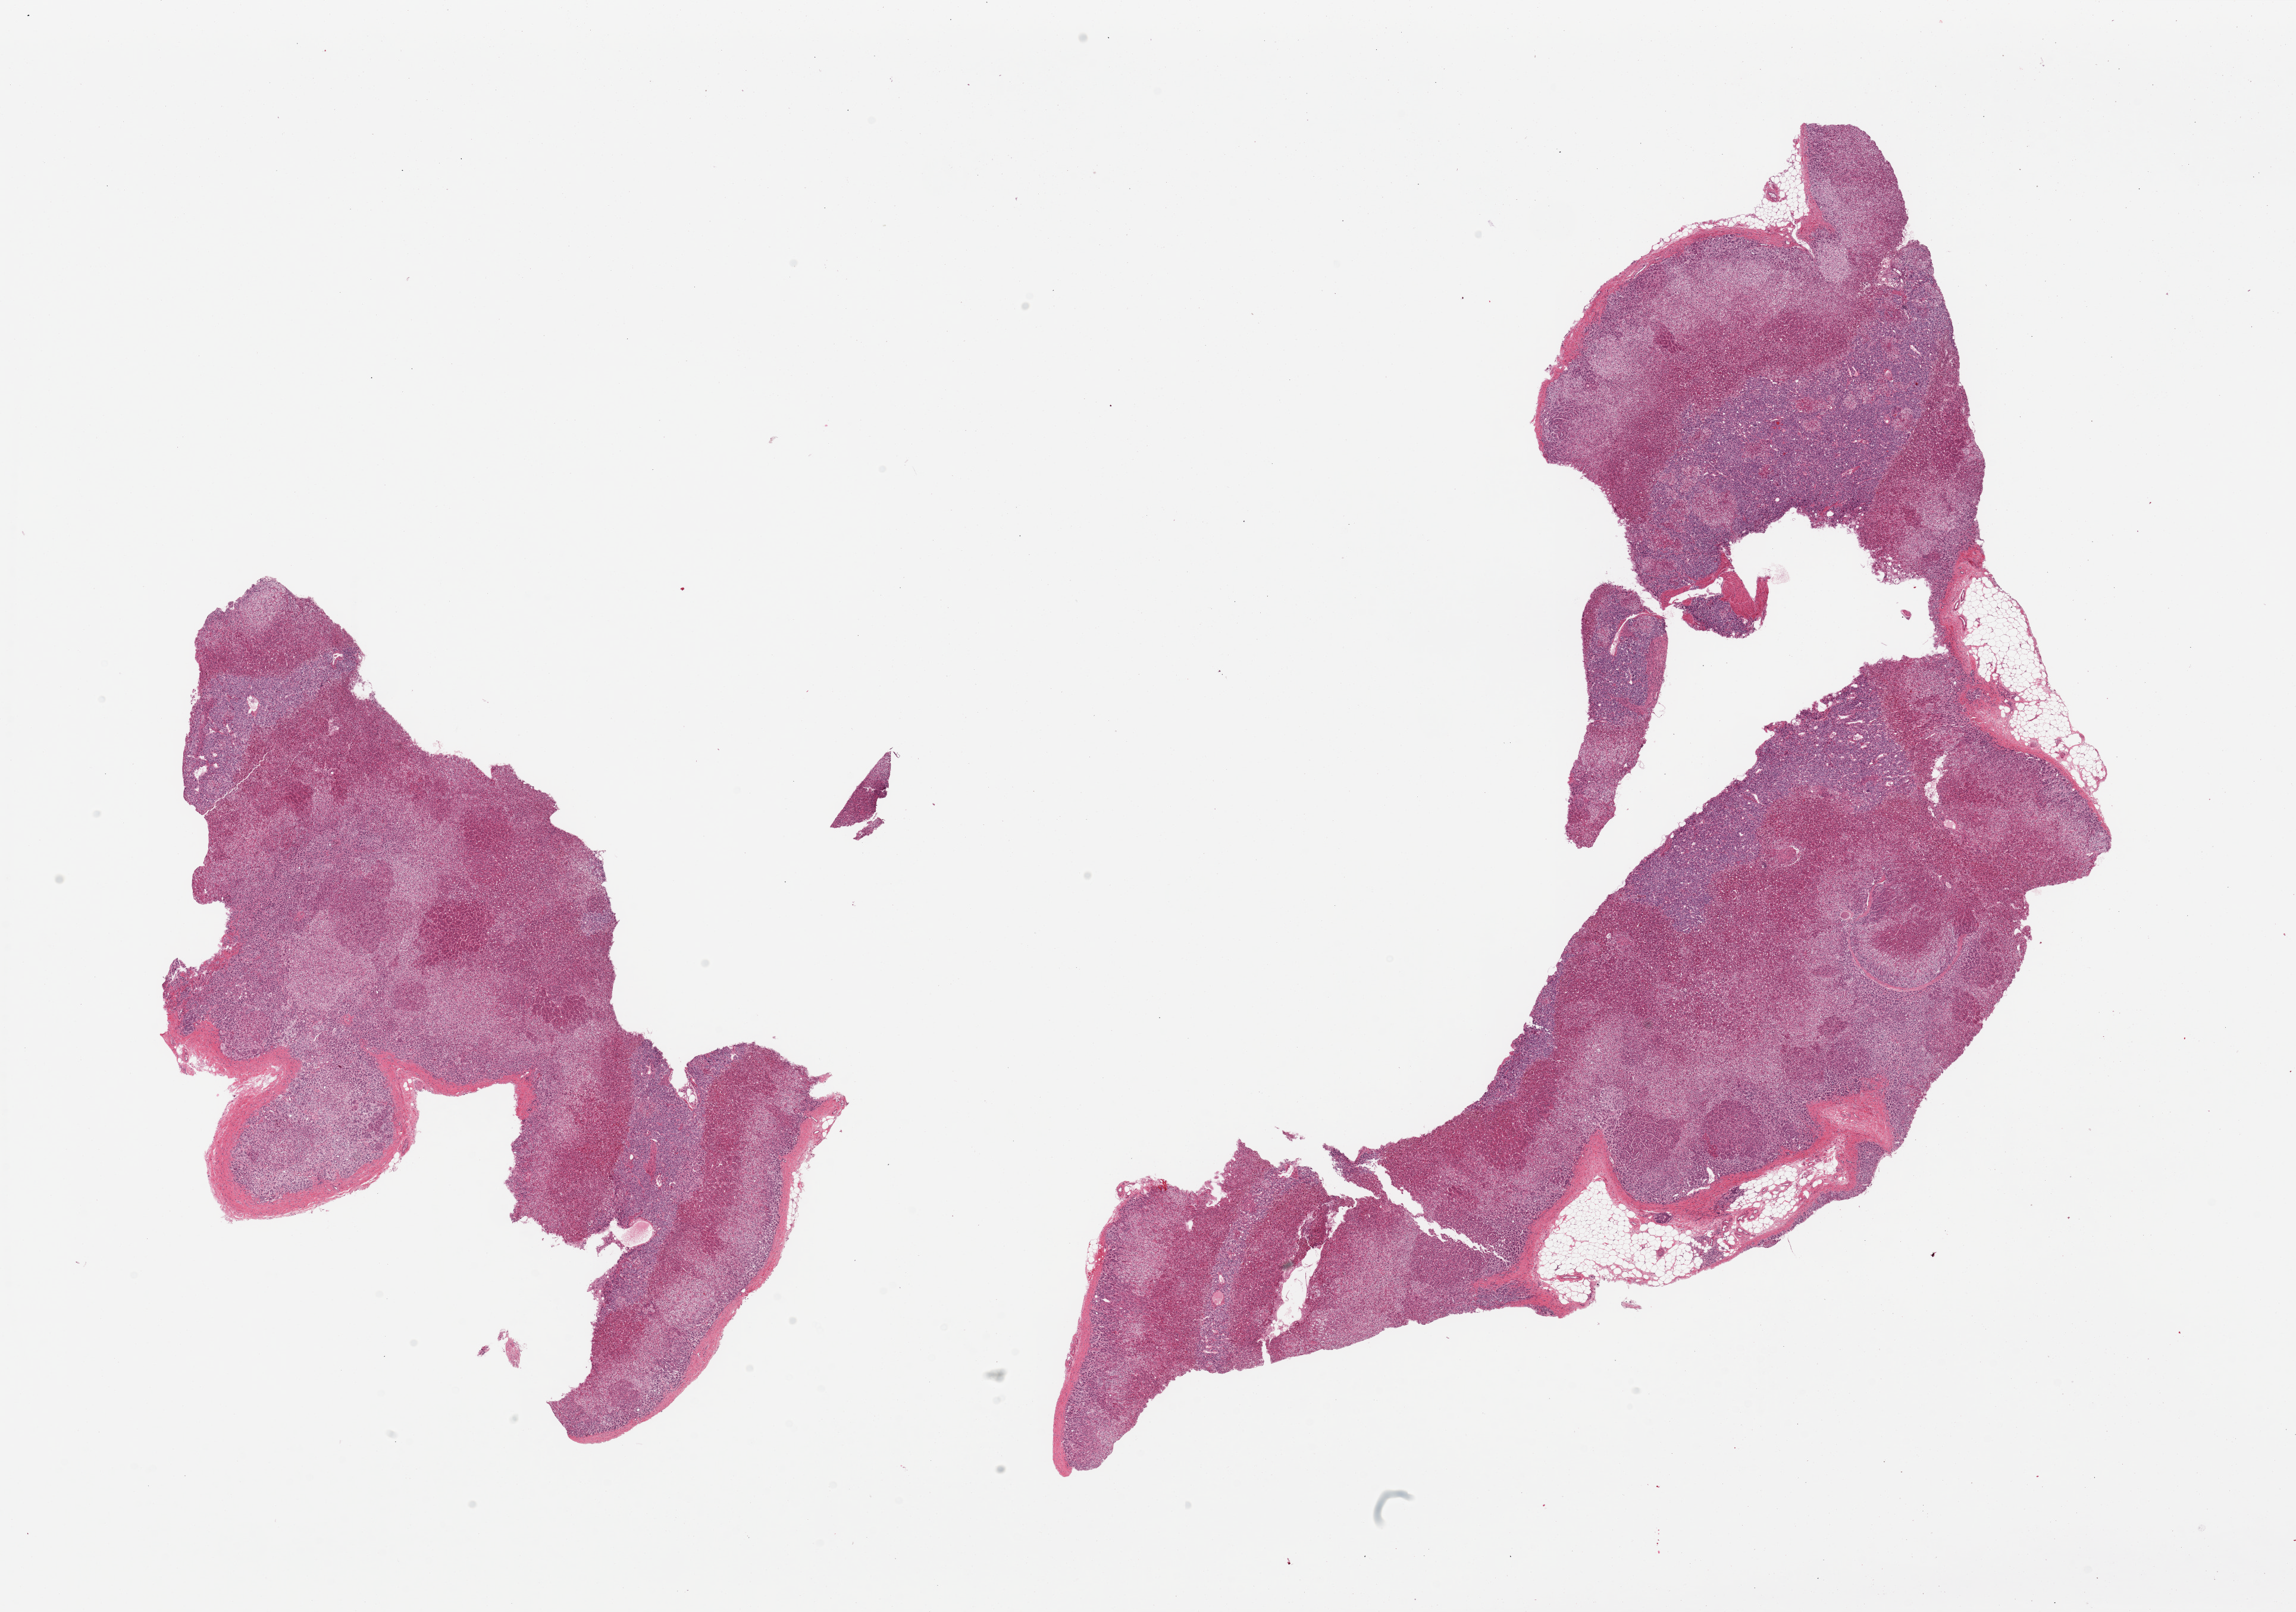
Digitized H&E-stained section — a low-resolution overview of the entire scanned area, about 30.5 x 21.4 mm (slide scanned at 20x), PAXgene-fixed, paraffin-embedded tissue, target tissue: adrenal gland, tissue donor sample. Donor: female.
Reviewer comment on this tissue sample: 2 pieces. <5% fat; medullary hyperplasia.